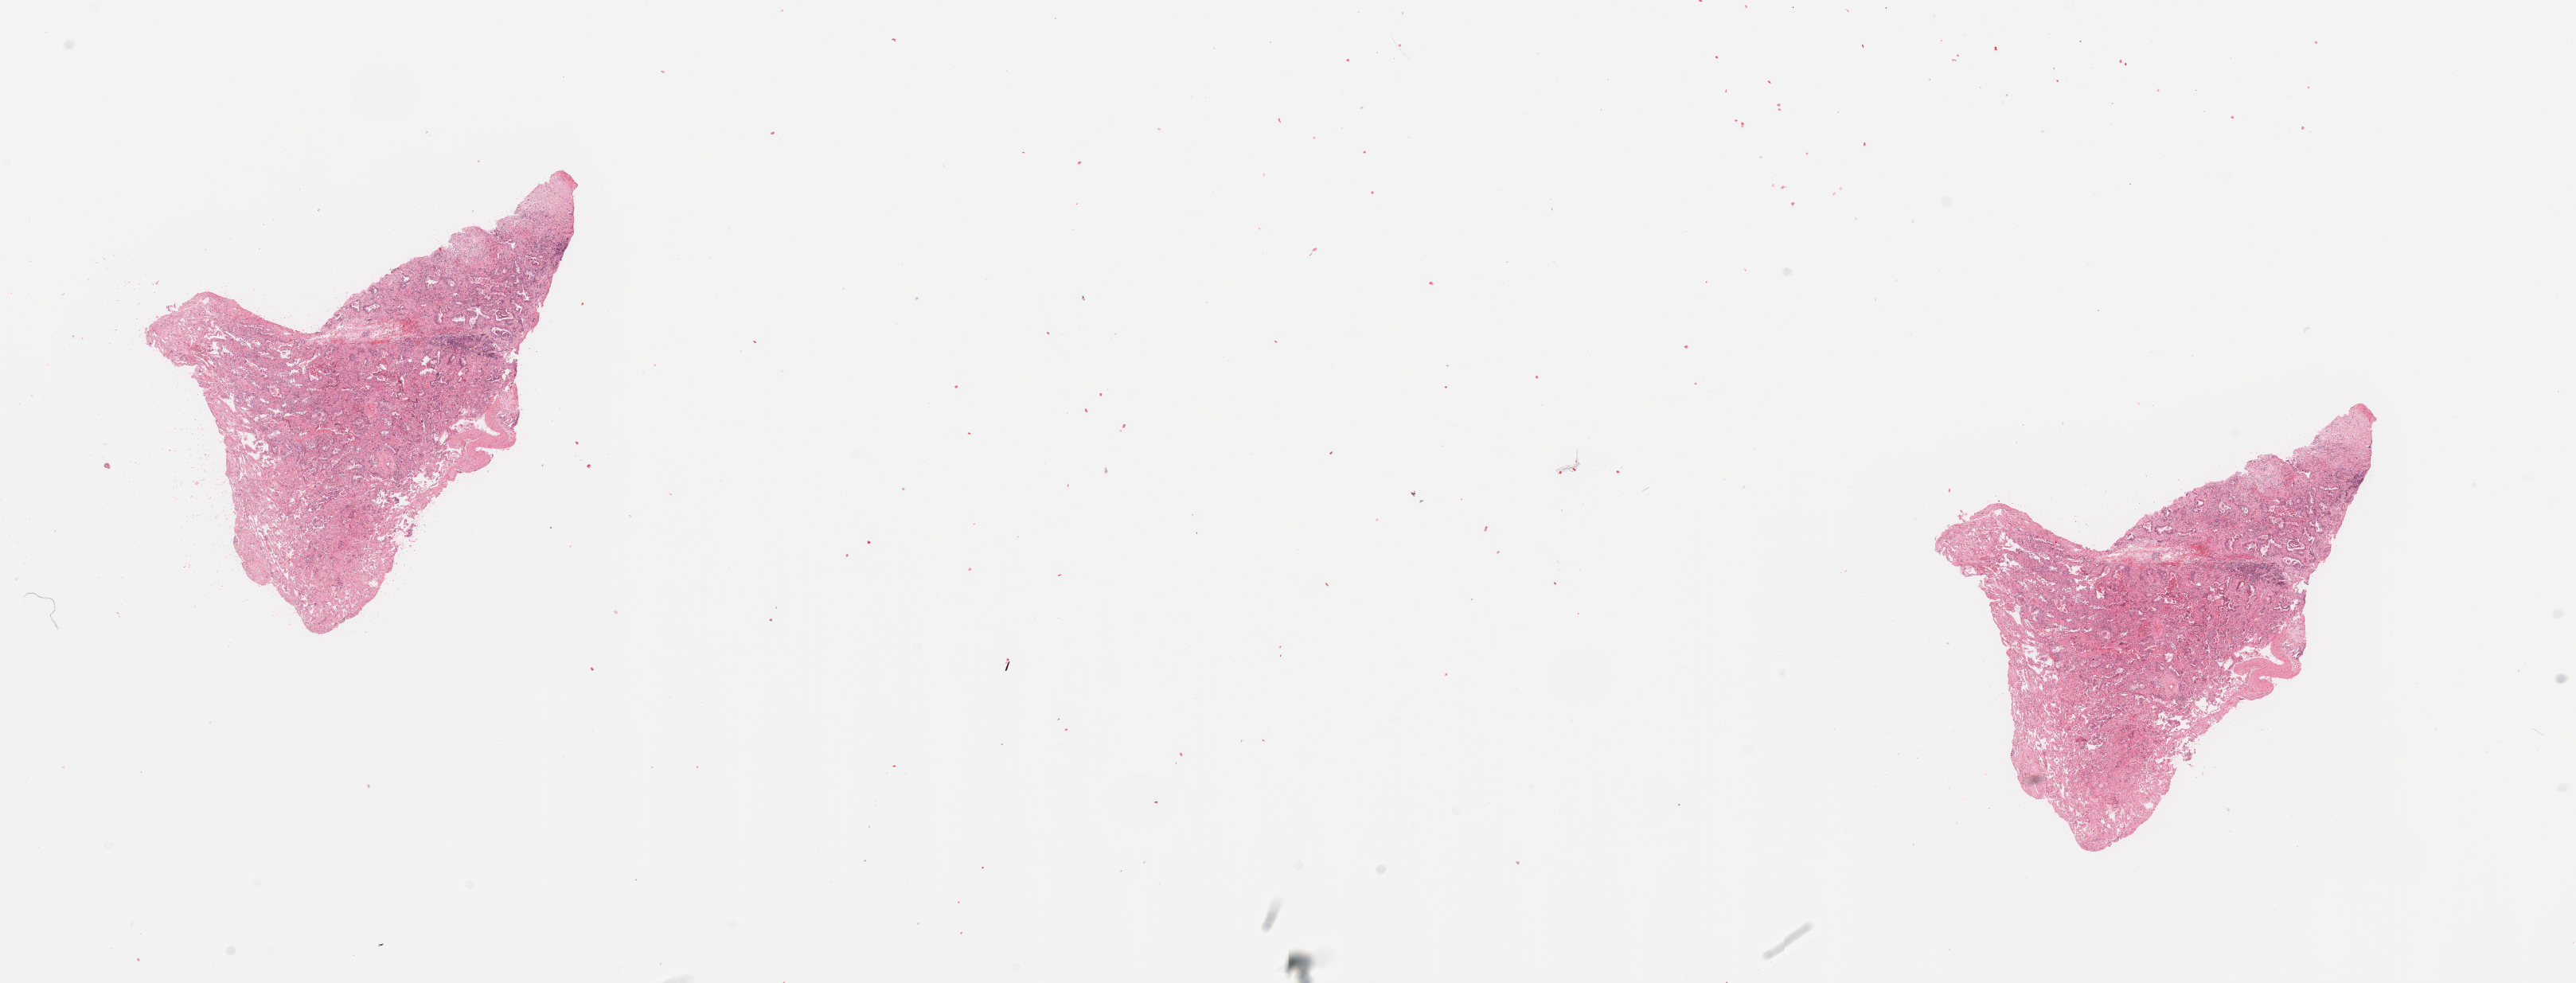
Whole-slide histology image, H&E-stained, low-resolution overview of the scanned area, about 25.6 x 9.8 mm (acquisition: 20x scan). Lung, tumour tissue. Female, 78 y/o. Histologic grade: G2 (moderately differentiated).
Histologic diagnosis: Adenocarcinoma, NOS. AJCC pathologic stage: IIB.